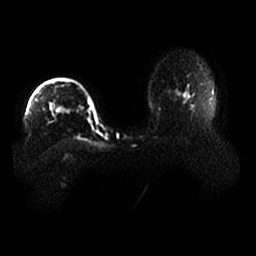
Breast MRI, one axial slice. Slice 33 of 33 in the series (ordered by position). Diffusion-weighted series; image 2 of 4 stored at this slice position (different b-values; order by instance number). 1.5 T. 4 mm slice thickness. 256 × 256 image matrix, field of view 400 × 400 mm. Female patient.
Outlined on this slice (manually delineated by an expert):
- tumour on diffusion-weighted imaging: bounding box <59,105,72,114> (left, top, right, bottom; pixels)